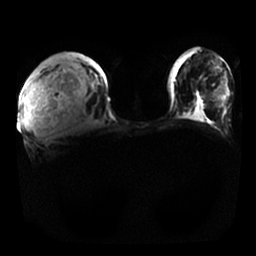
Breast MRI, one axial slice. Position 7 of 25 along the scan axis. Diffusion-weighted series; image 2 of 4 stored at this slice position (different b-values; order by instance number). 1.5 T. 4 mm slice thickness. 256 × 256 image matrix, field of view 350 × 350 mm. Female patient.
Annotated regions visible in this slice (expert manual segmentation):
- tumour on diffusion-weighted imaging: bounding box (x1, y1, x2, y2) in pixels: (25, 72, 52, 137)